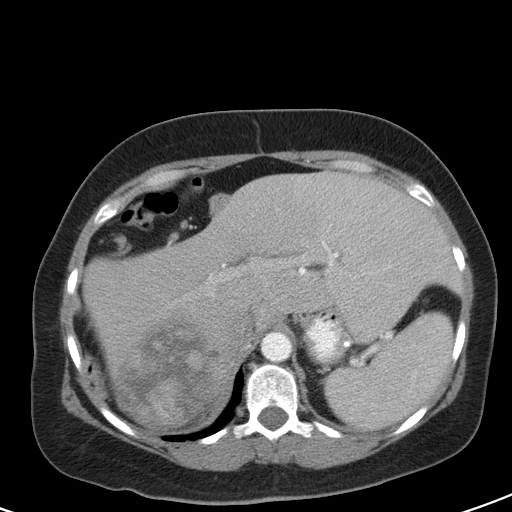
Contrast-enhanced abdominal CT, one axial slice; slice 78 of 126 in the series (ordered by position); 120 kVp; intravenous contrast given; soft-tissue window (W 400 / L 40 HU); 5 mm slice thickness; 512 × 512 image matrix. Female patient, age 51 years. Case-level facts recorded for this patient, not image findings: diagnosis: adrenocortical carcinoma; tumour side: right adrenal; tumour size at pathology: 17 cm; Ki-67 index: 12 %; stage (as recorded): 2.
Structures marked on this image (semi-automatic segmentation, software-assisted and operator-edited):
- mass: box from (x=117, y=312) to (x=209, y=426) px